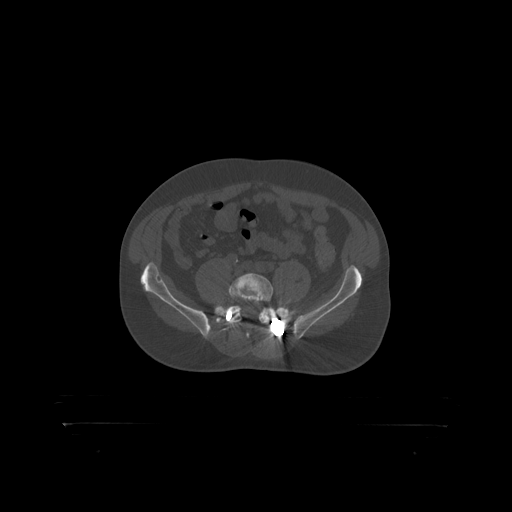
CT including the spine, one axial slice. Position 196 of 399 along the scan axis. 120 kVp. Bone window (W 1800 / L 400 HU). 1.25 mm slice thickness. 512 × 512 image matrix. Male patient, age 46 years. Case-level facts recorded for this patient, not image findings: primary cancer: skin.
Outlined on this slice (semi-automatic segmentation, software-assisted and operator-edited):
- L5 vertebra: bounding box <229,273,274,319> (left, top, right, bottom; pixels)